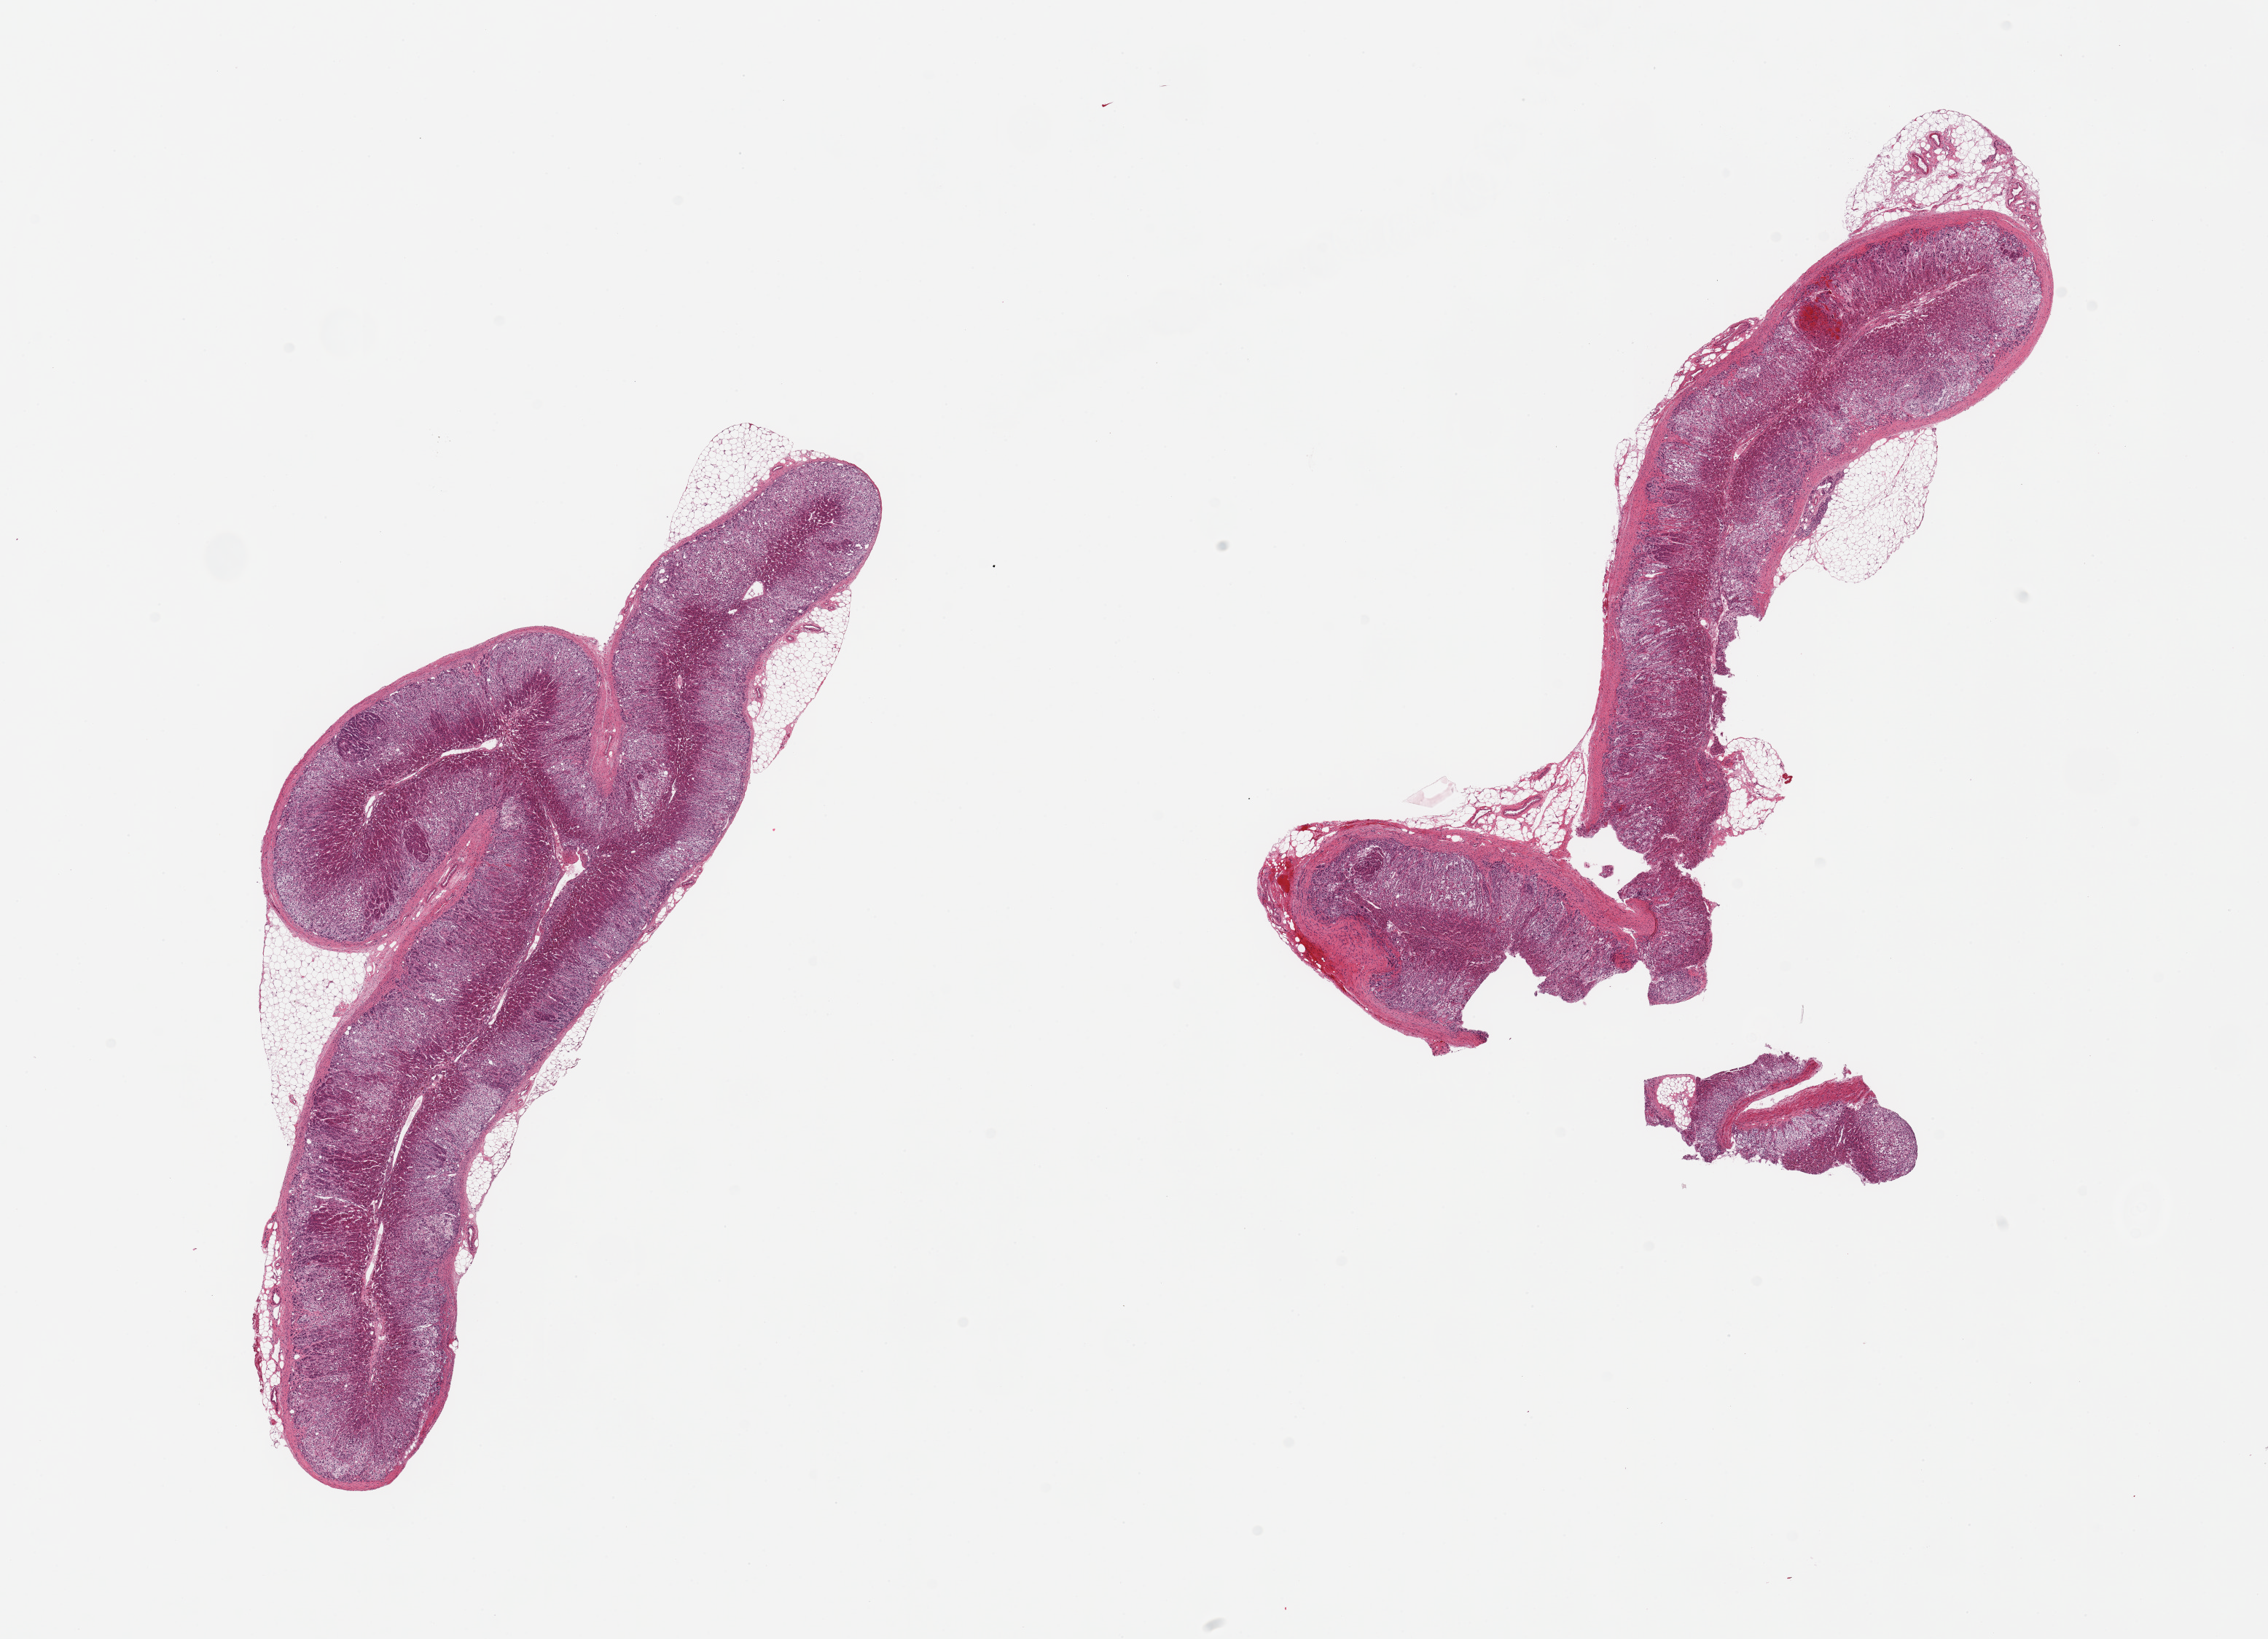
Haematoxylin and eosin whole-slide image, a low-resolution overview of the entire scanned area, about 24.6 x 17.8 mm. PAXgene-fixed, paraffin-embedded tissue. Sampled site (target tissue): adrenal gland. Tissue donor sample. Donor: female.
* pathologist's review note for this sample: 2 pieces; 5-10% attached fat on both